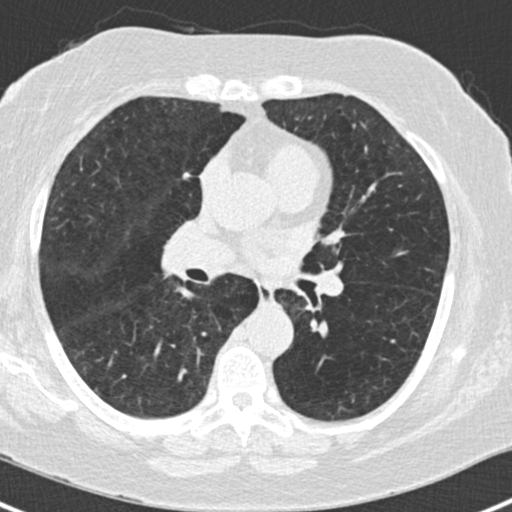
Low-dose screening chest CT, one axial slice; slice 82 of 168 in the series (ordered by position); reconstruction kernel B30f; 120 kVp; lung window (W 1500 / L -600 HU); 2 mm slice thickness; 512 × 512 image matrix, field of view 303 × 303 mm.
Outlined on this slice (outlined manually by an expert reader):
- lesion 1 (tumor, upper lobe of right lung): bounding box [x1, y1, x2, y2] px = [183, 172, 200, 179]